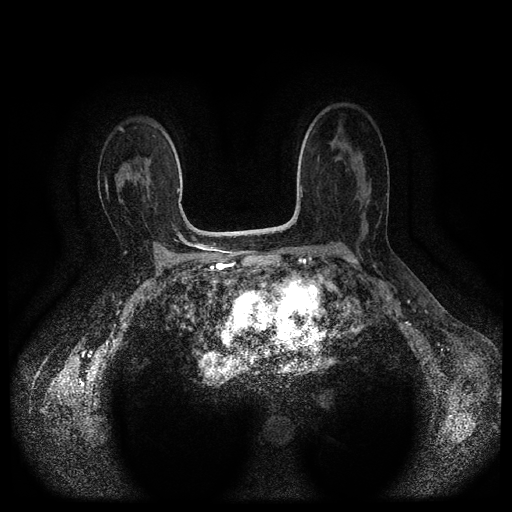
Breast MRI (dynamic contrast-enhanced, multi-phase), one axial slice. Dynamic contrast-enhanced series, time point 2 of 5 at this slice position (early post-contrast). 1.5 T. TE 2.6 ms, TR 5.4 ms. 2 mm slice thickness. 512 × 512 image matrix. Patient: female, 53 years.
Structures marked on this image (semi-automatic segmentation, software-assisted and operator-edited):
- breast lesion (labelled 'tumour' in the annotation; benign lesions carry a separate 'benign' label): bounding box <141,186,153,201> (left, top, right, bottom; pixels)